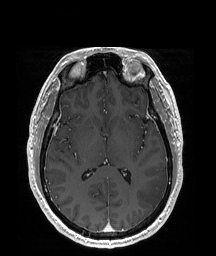
Brain MRI from a brain-tumour surgery series, one axial slice; position 97 of 192 along the scan axis; T1-weighted post-contrast; 1 mm slice thickness; 216 × 256 image matrix, field of view 219 × 260 mm. Case-level facts recorded for this patient, not image findings: histopathology: Glioblastoma; WHO grade: 4; IDH mutation: no.
Annotated regions visible in this slice (outlined manually by an expert reader):
- tumour: bounding box (x1, y1, x2, y2) in pixels: (138, 172, 168, 210)